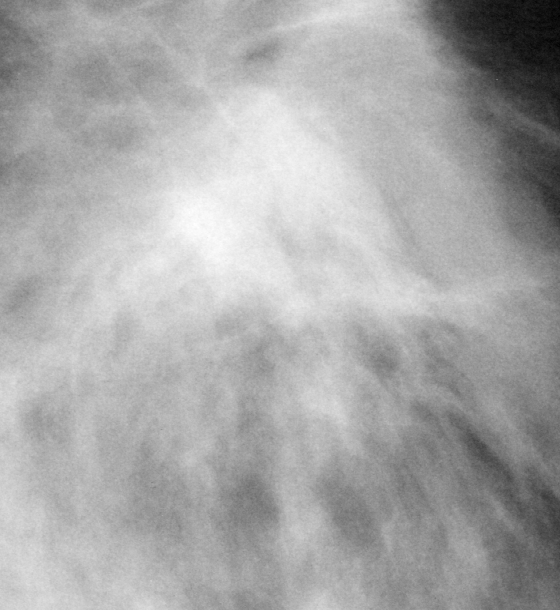
Region of interest cut from a scanned film mammogram (one marked finding), left breast, MLO view.
Marked abnormality: mass, shape irregular / architectural distortion, margins ill defined / spiculated; BI-RADS assessment category 4; subtlety rating 4 on a 1 (subtle) to 5 (obvious) scale; pathology result (as recorded, not read from the image): malignant.